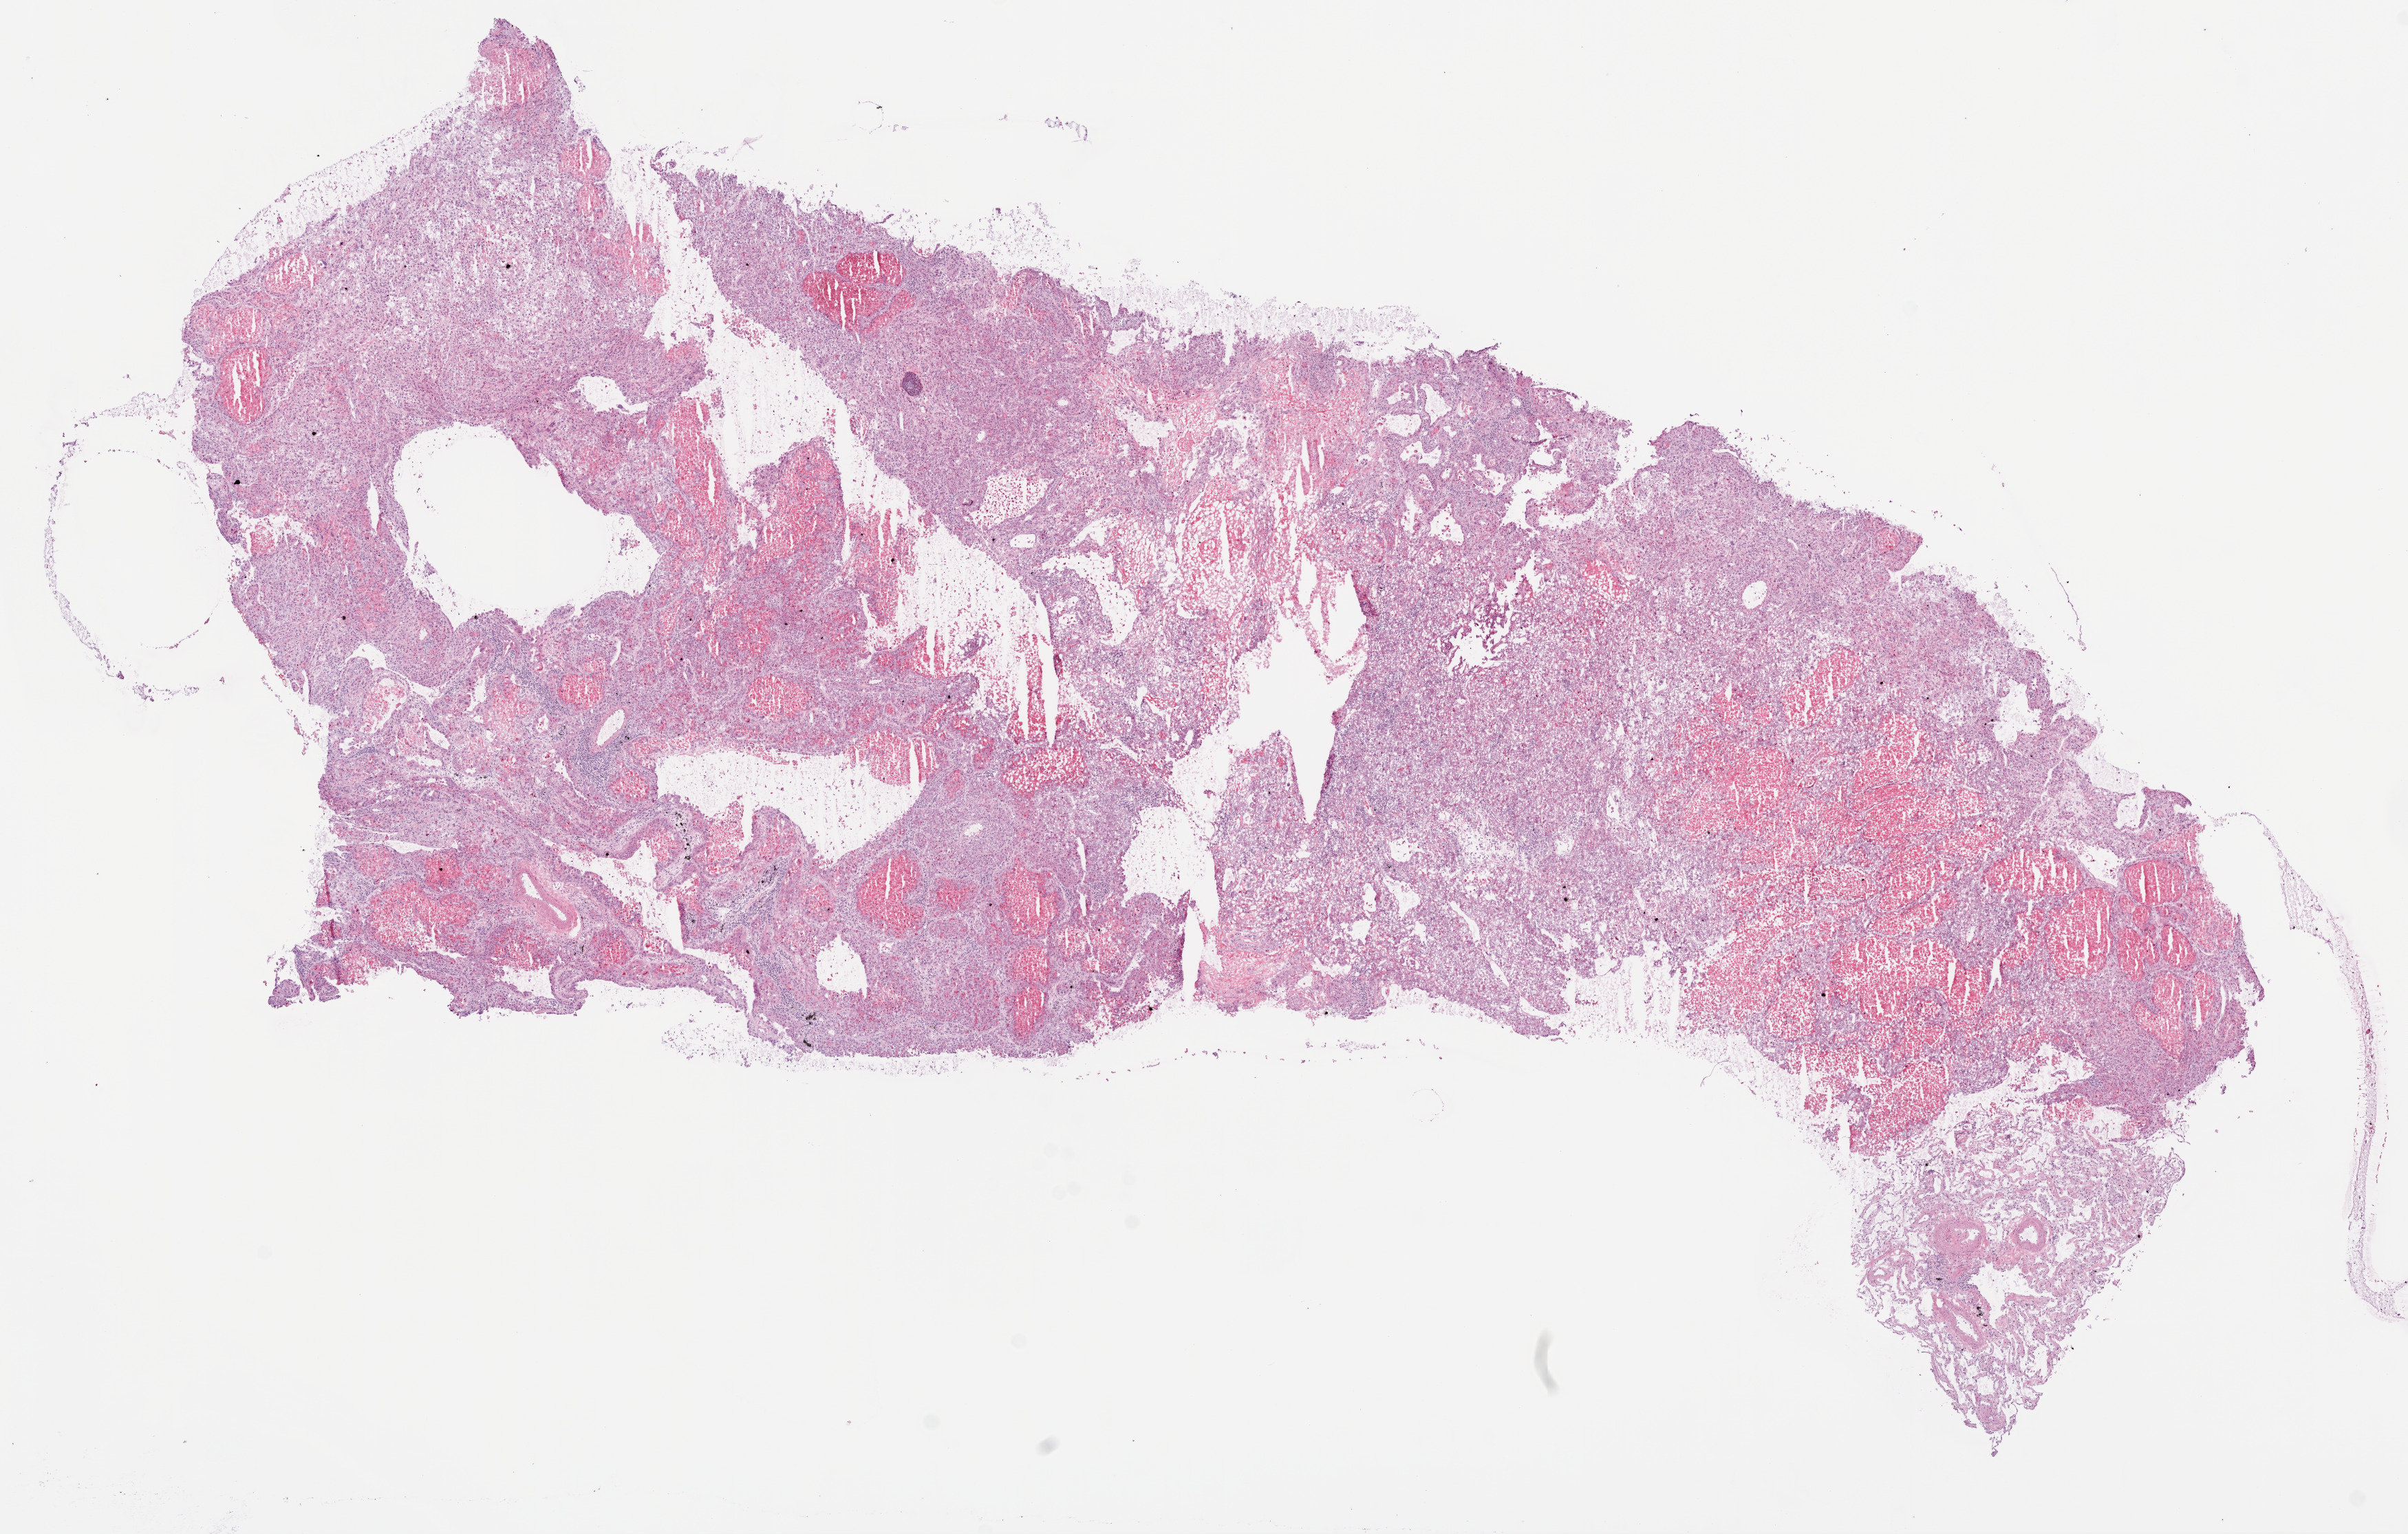
Whole-slide histology image, H&E-stained, low-resolution overview of the scanned area, about 14.0 x 8.9 mm (from a 20x scan), frozen section, lung, primary tumour sample. Male, age 59 years at initial diagnosis.
Histologic diagnosis: Squamous cell carcinoma, NOS (upper lobe, lung).